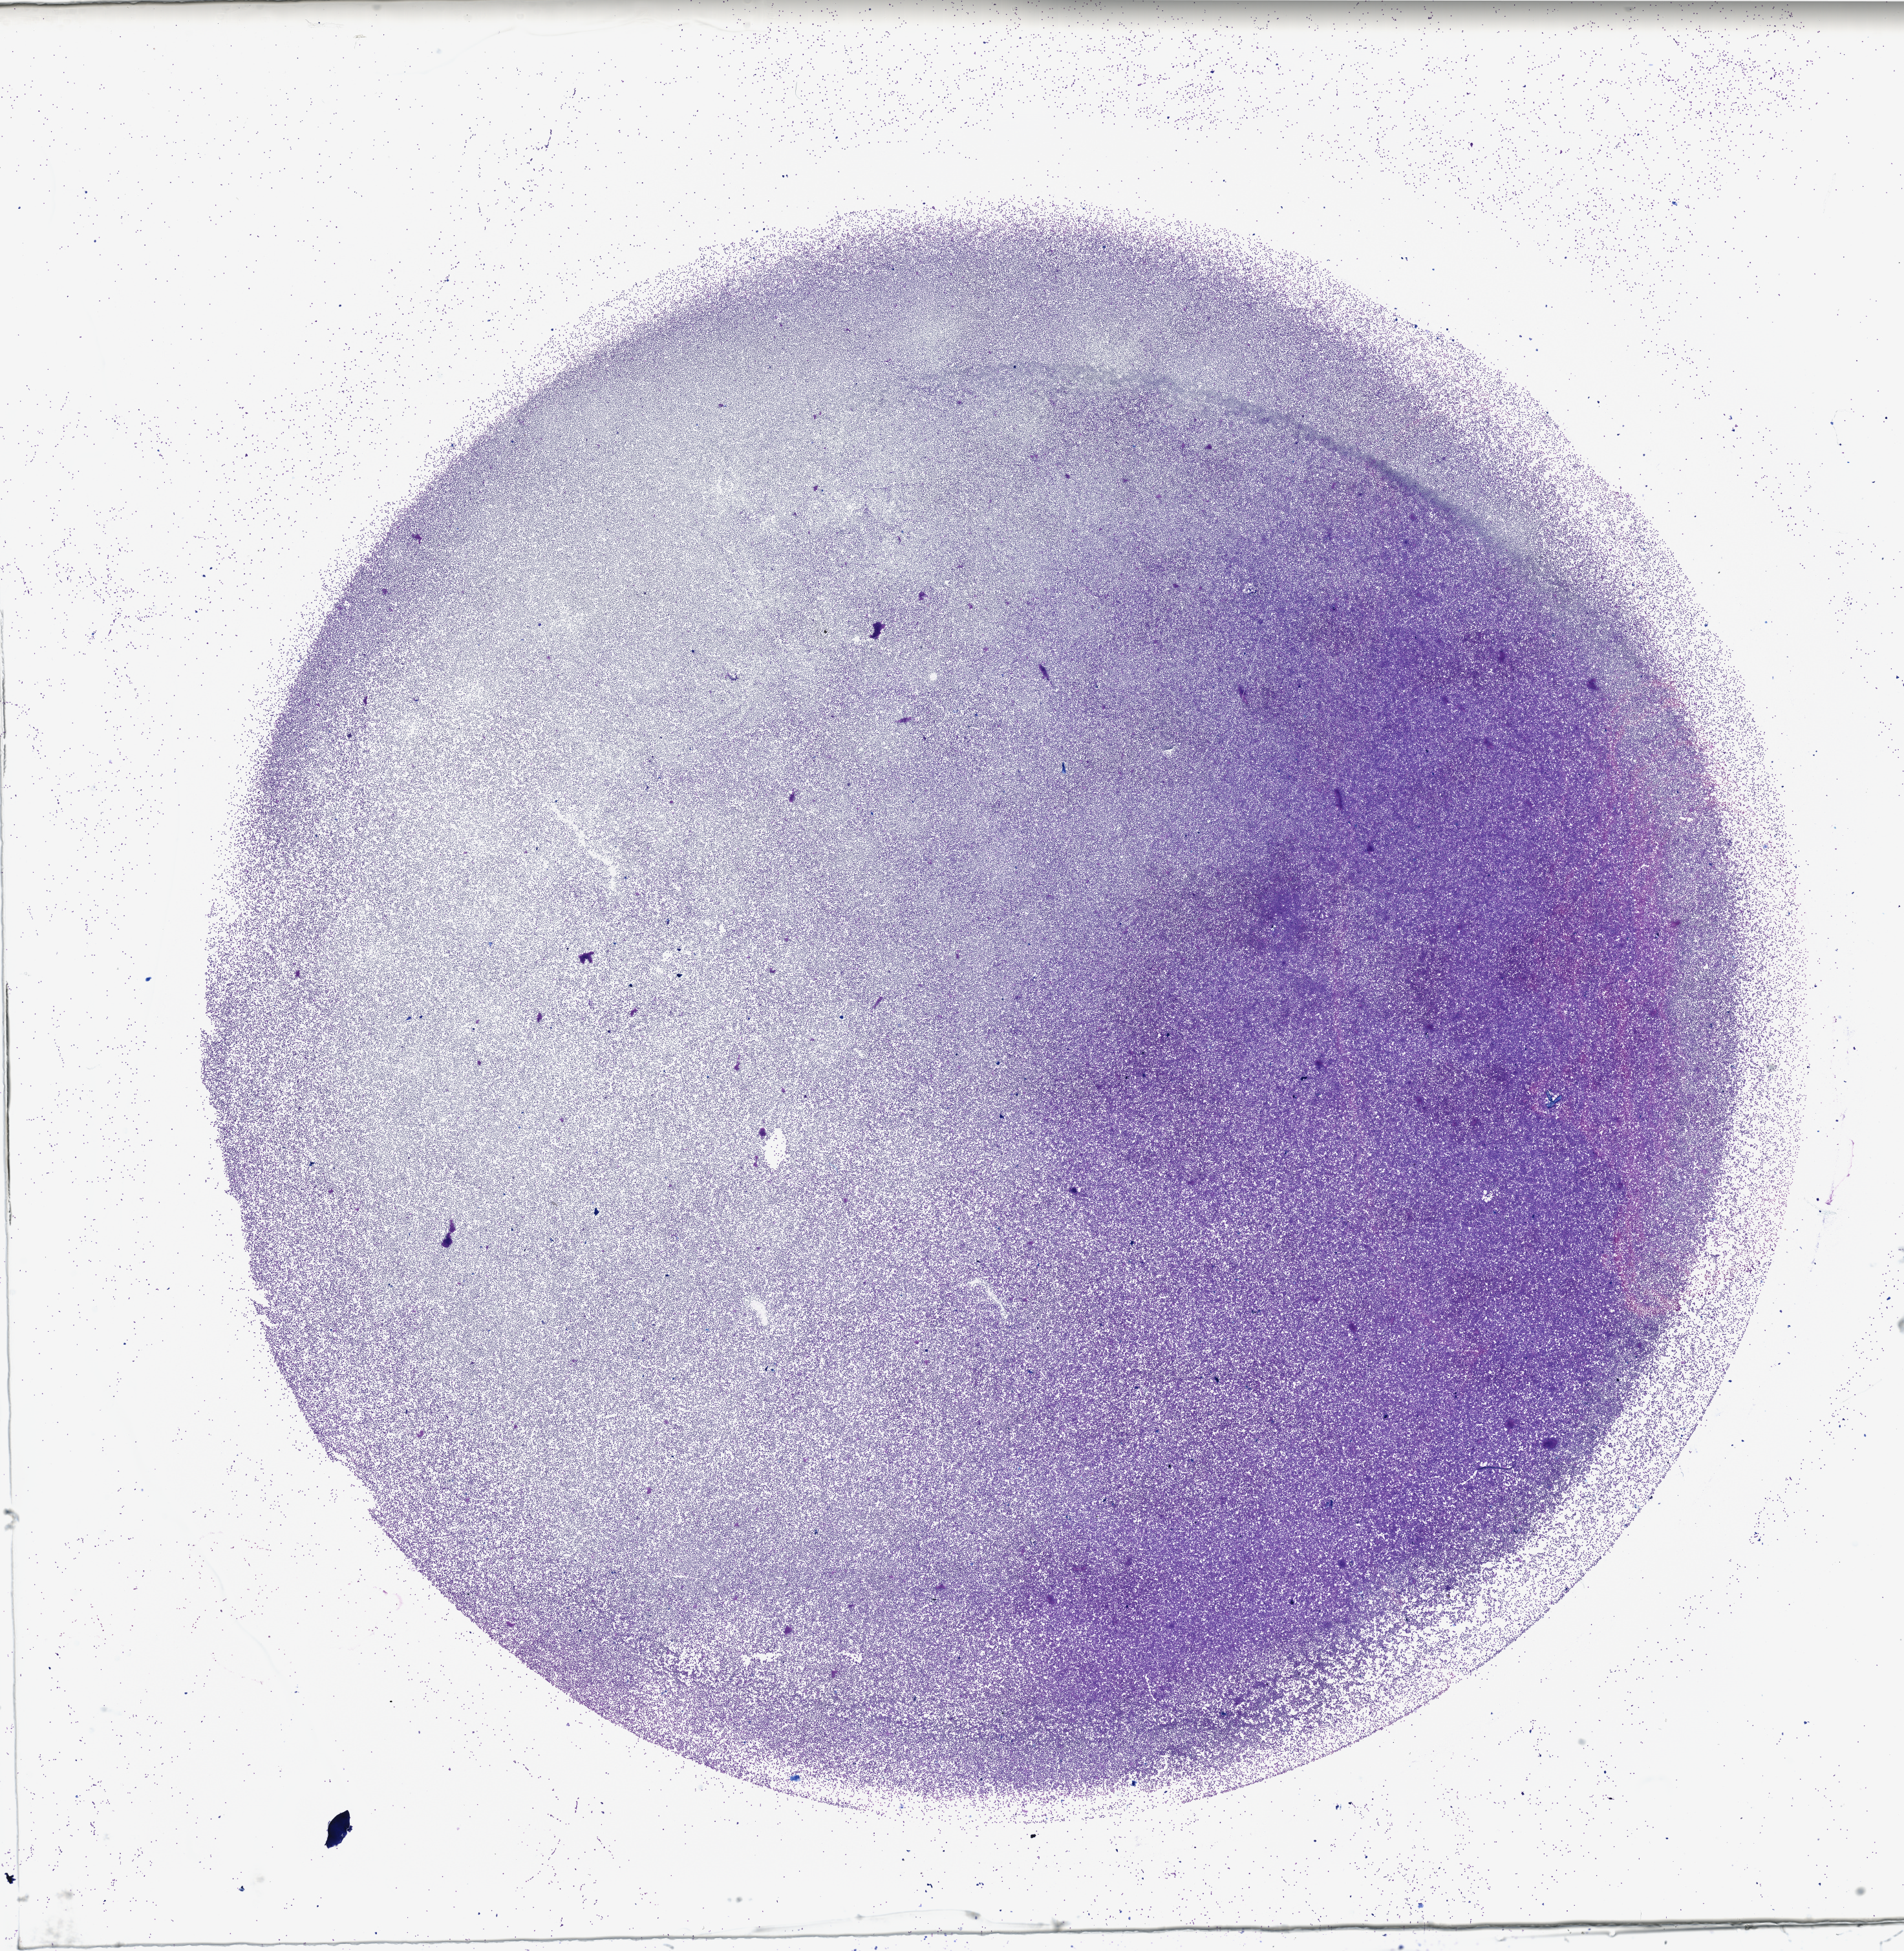
Whole-slide histology image, Hematoxylin and eosin (H&E) stained, shown as a low-resolution overview of the whole scanned area (about 23.3 x 23.8 mm). Bone marrow (leukaemic) sample. Patient: male, age 65 years. Blasts: 95%.
• WHO classification: AML with maturation
• diagnosis: Acute Myeloid Leukemia
• FAB classification: M2